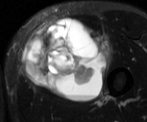
MRI of an extremity soft-tissue mass, one axial slice; slice 27 of 52 in the series (ordered by position); T2-weighted fat-saturated; MR volume resampled by the dataset authors to the PET/CT grid (not the native acquisition matrix); 3.27 mm slice thickness; 147 × 122 image matrix. Male patient. Case-level facts recorded for this patient, not image findings: histological type: pleiomorphic liposarcoma; grade: high; site of the primary tumour: left thigh.
Structures marked on this image (expert contour drawn on MRI and transferred to this co-registered scan by the dataset authors):
- gross tumour volume including surrounding oedema: bounding box <21,16,115,102> (left, top, right, bottom; pixels)
- gross tumour volume (mass): <21,16,110,102>